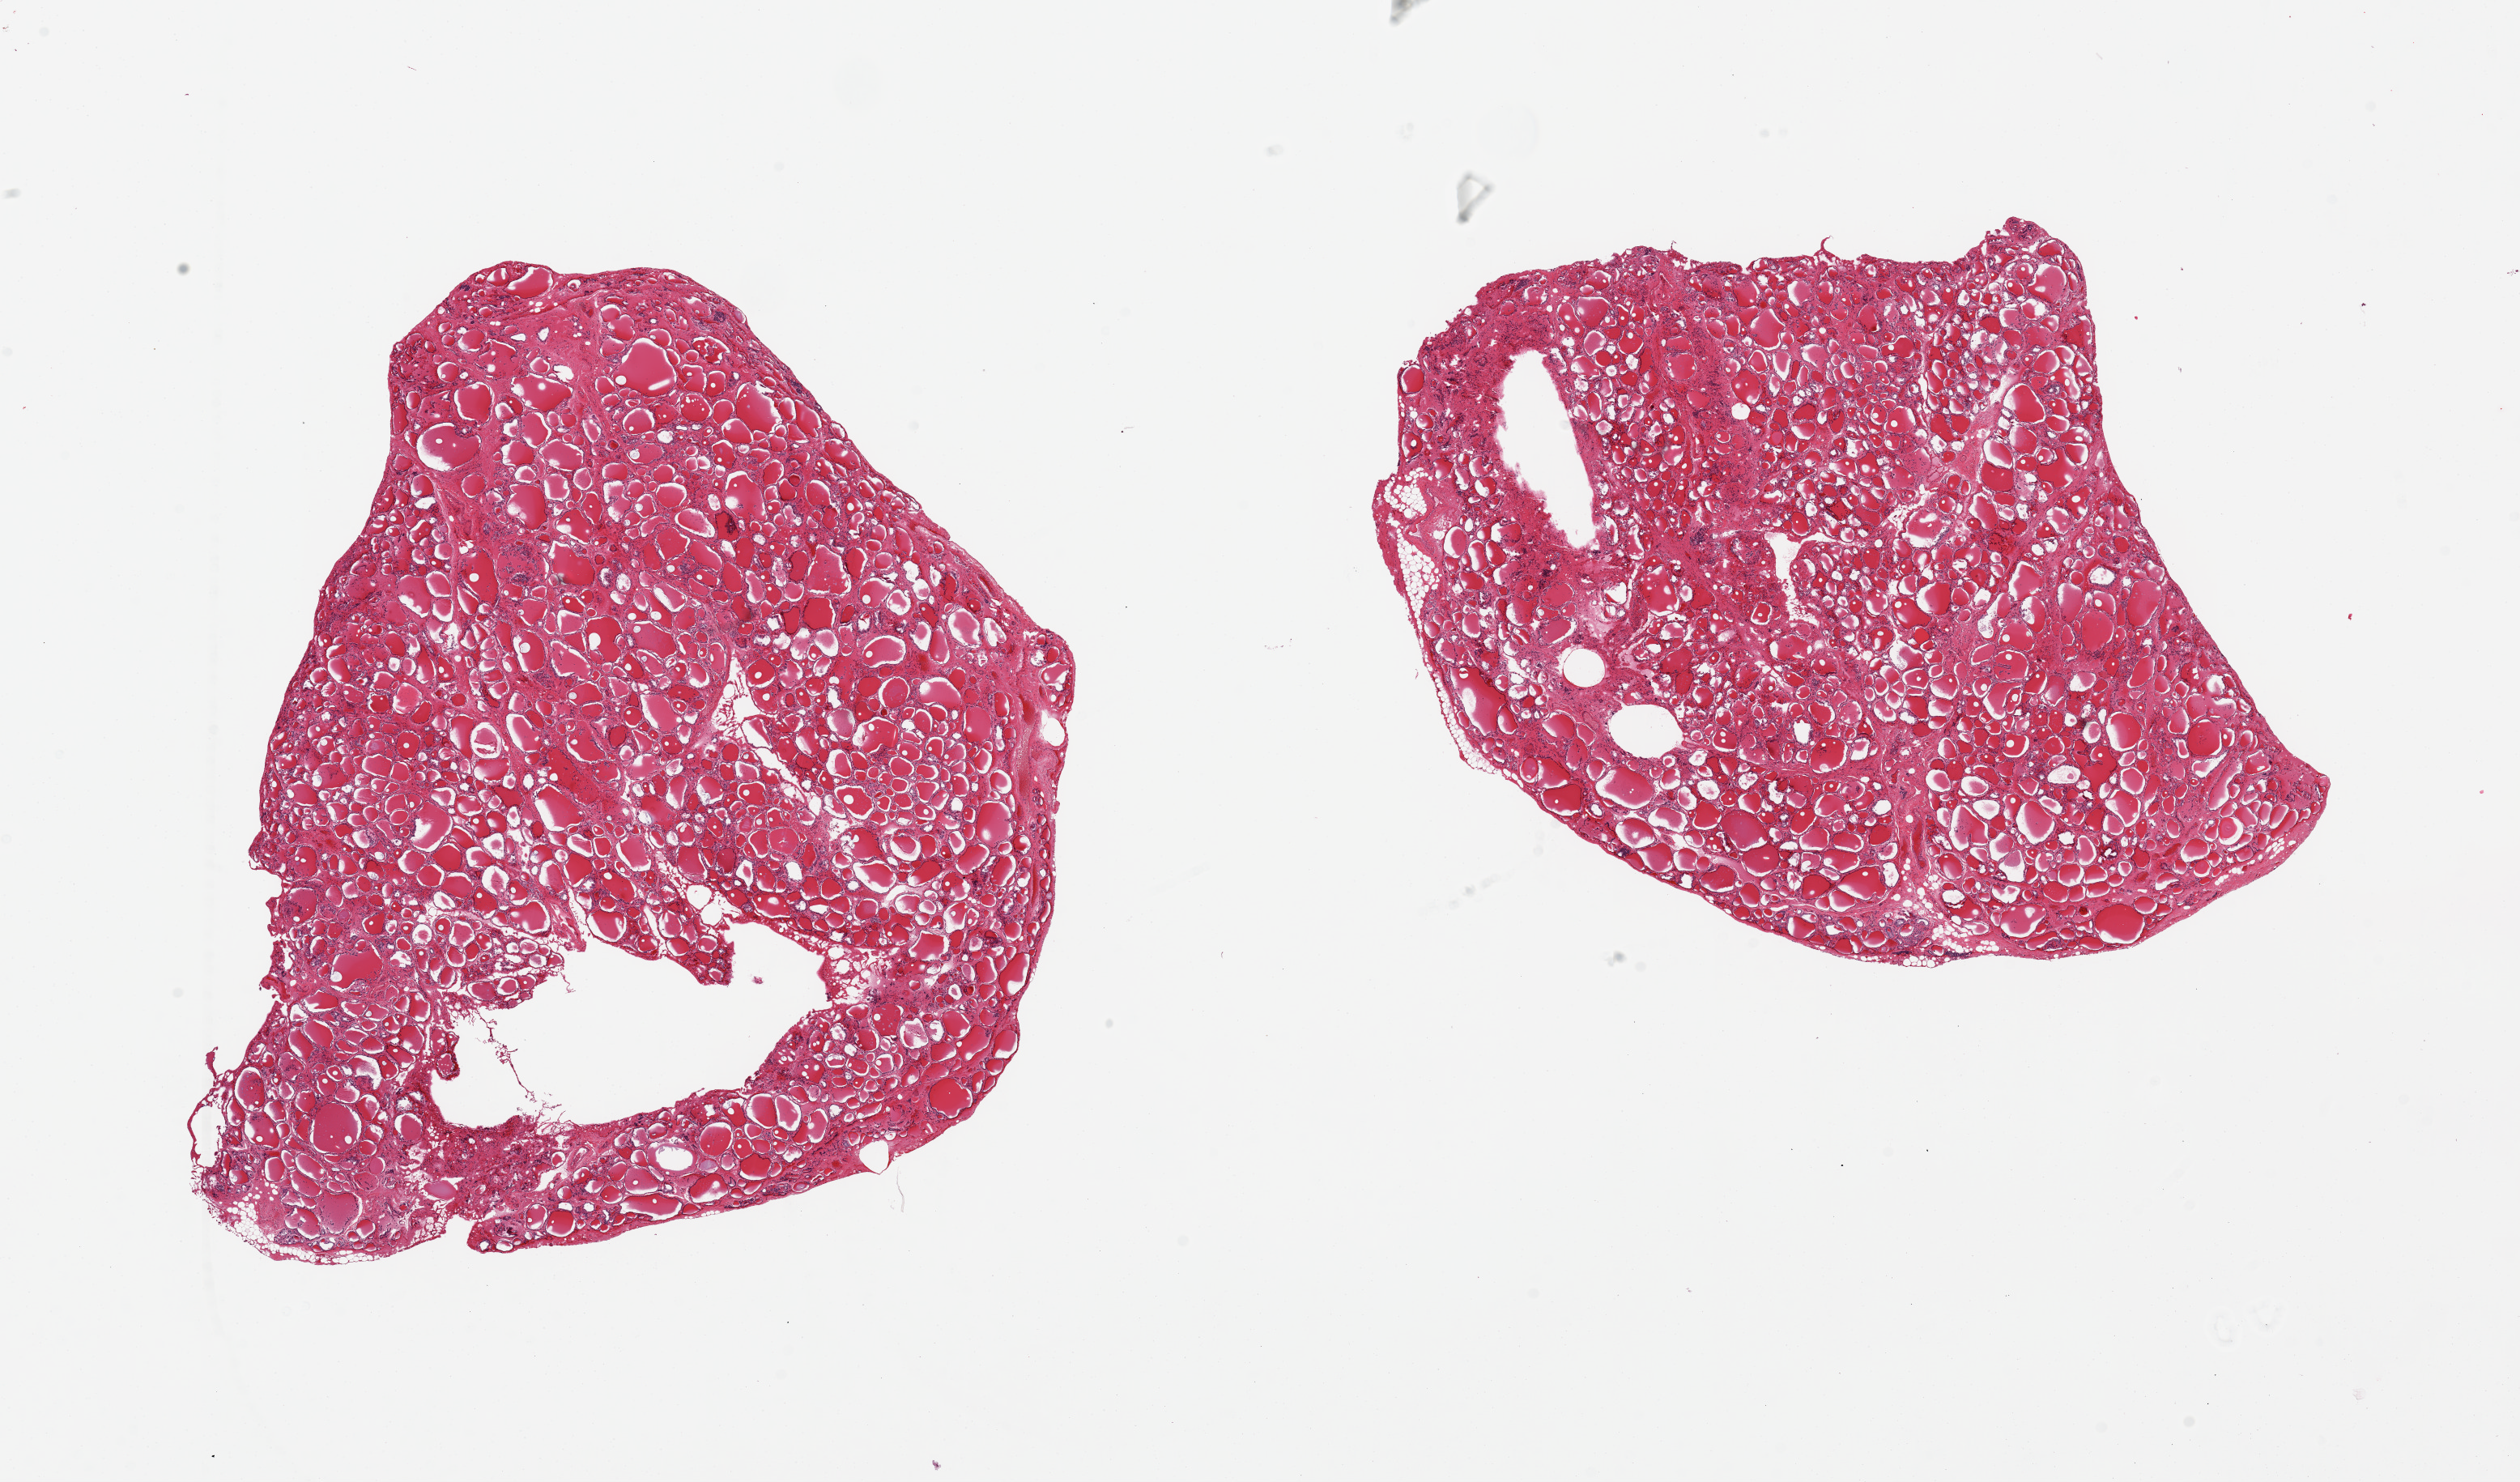
Whole-slide image, H&E stain, brightfield — whole scanned area (about 24.6 x 14.5 mm, acquisition: 20x scan) shown as a low-resolution overview; PAXgene-fixed, paraffin-embedded tissue; sampled site (target tissue): thyroid; donor tissue sample.
Pathologist's review note for this sample: 2 pieces, incidental simple cysts.